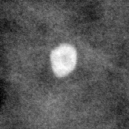
Crop from a digitized film mammogram around one marked abnormality, right breast, MLO view.
- Finding: calcifications, morphology coarse / round and regular / lucent centered; BI-RADS assessment category 2; subtlety rating 4 on a 1 (subtle) to 5 (obvious) scale; benign without callback (not worked up further).